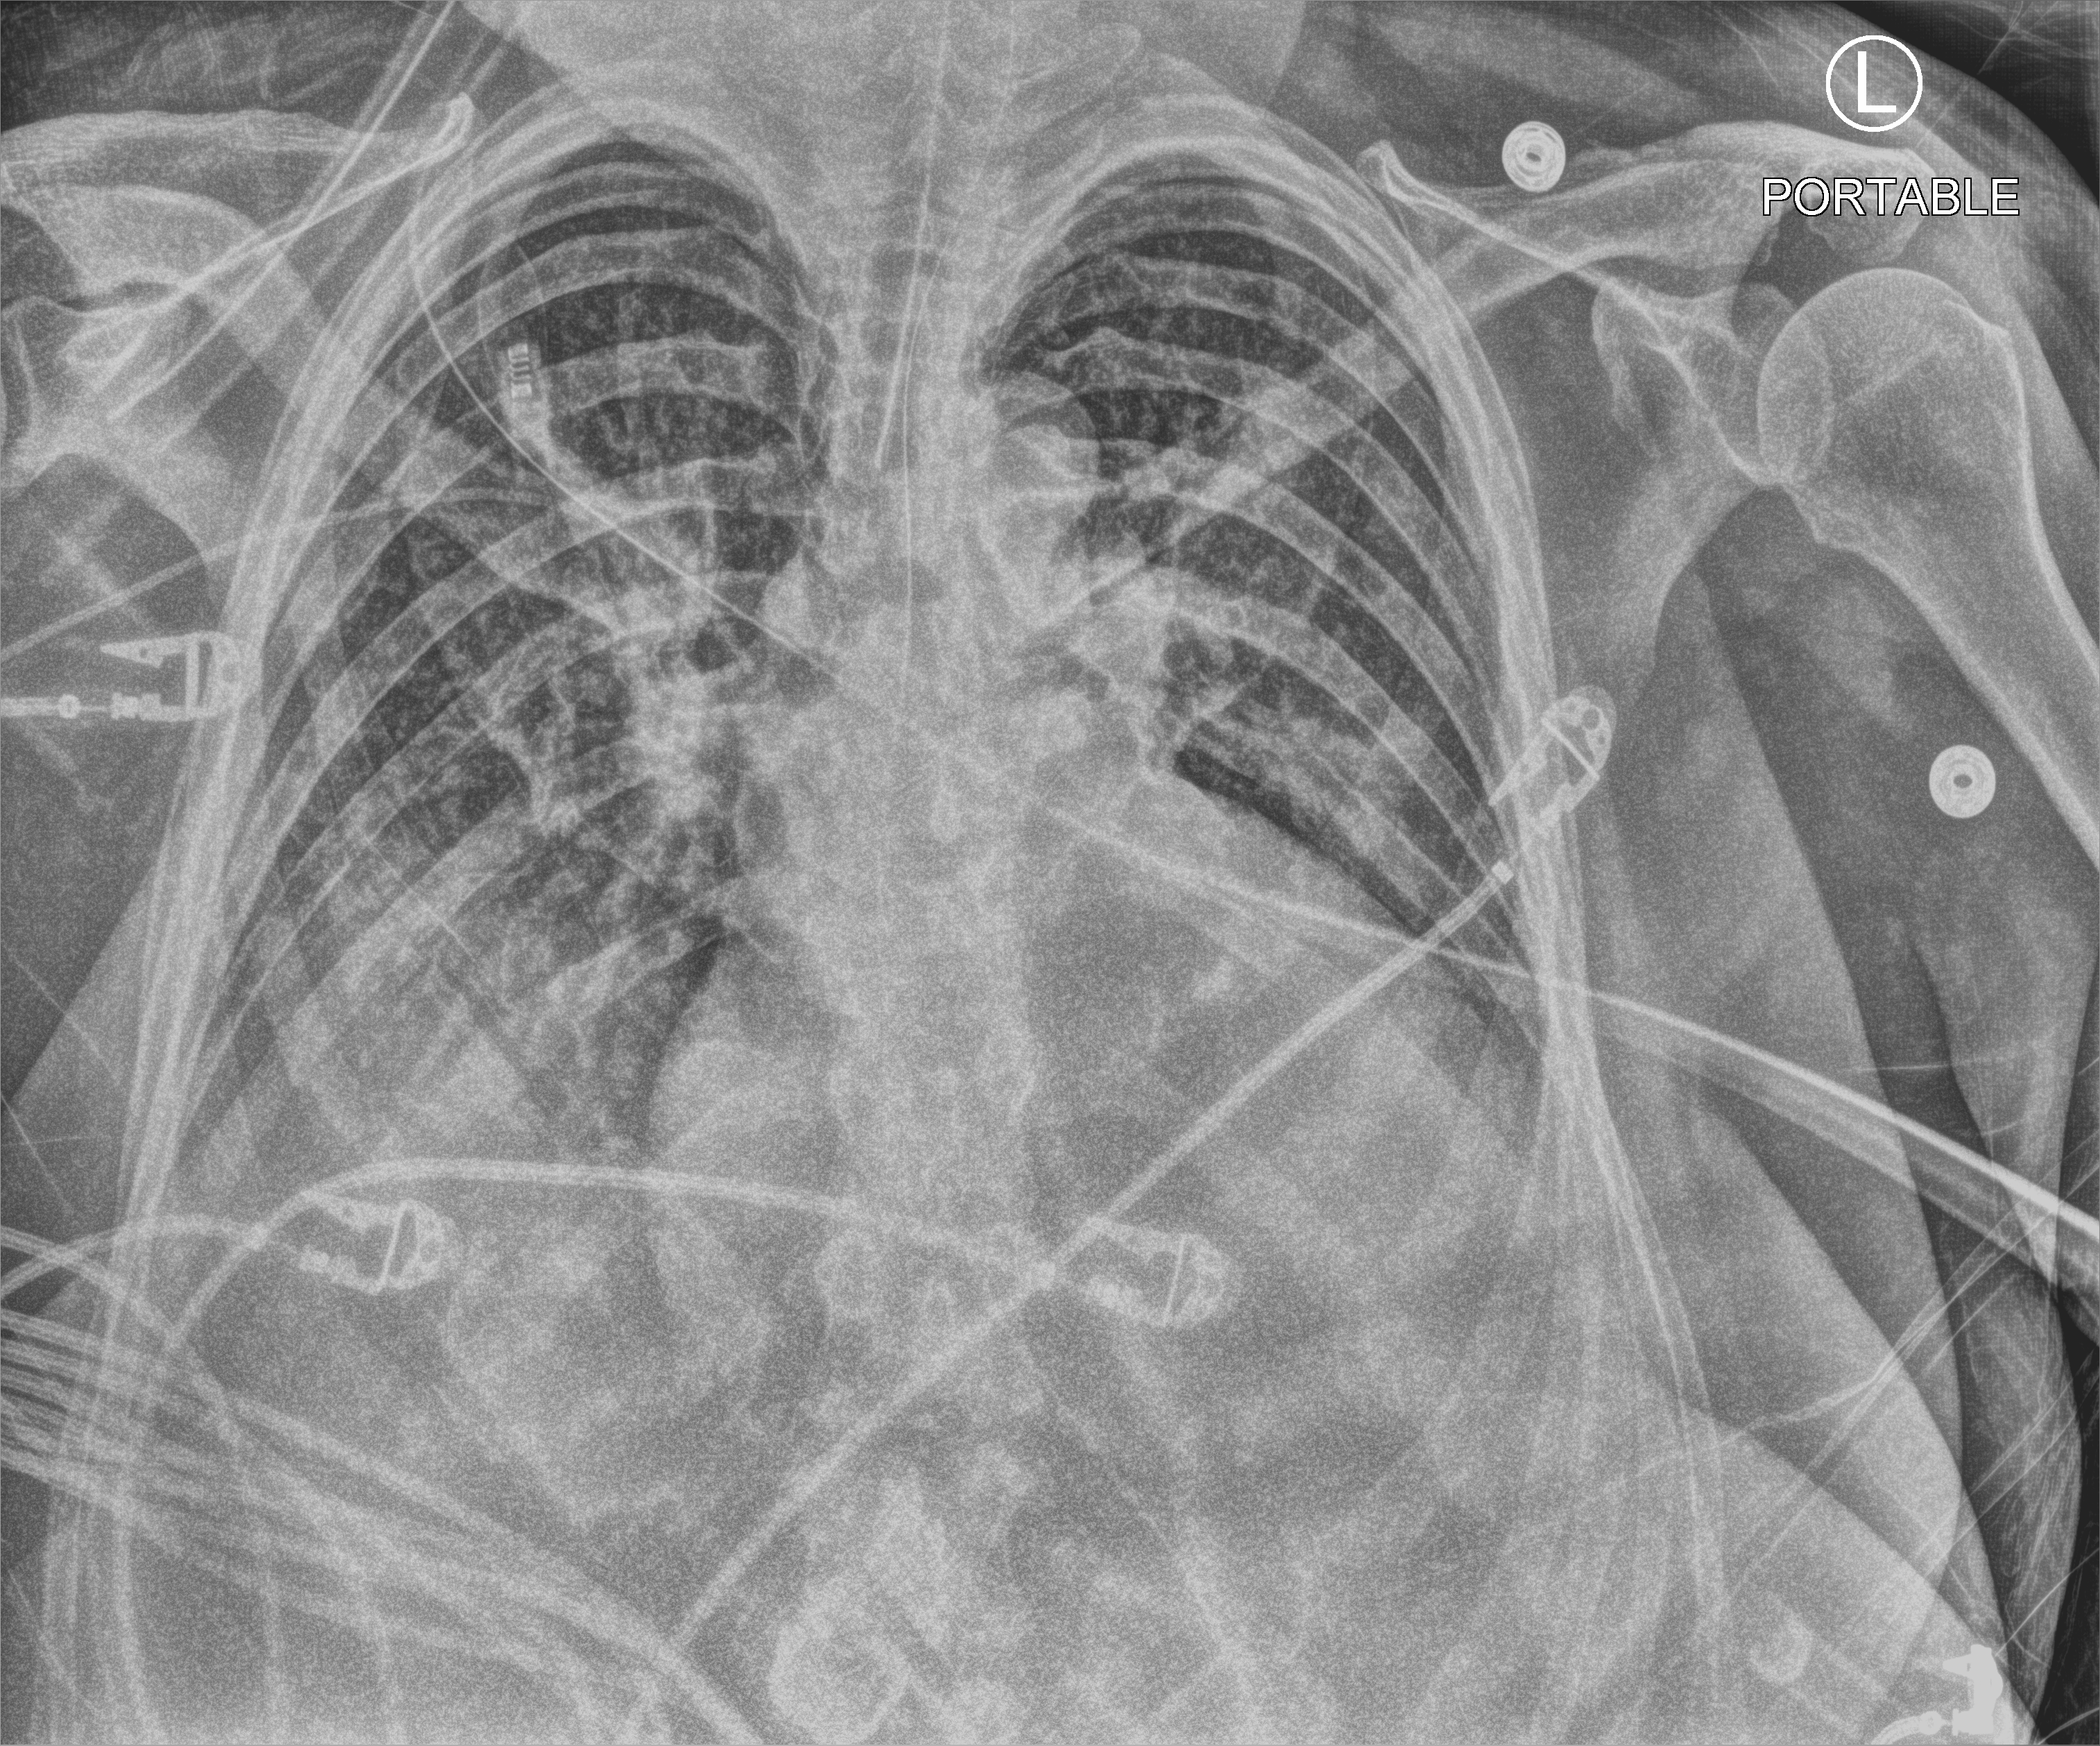
Portable chest radiograph. Female patient hospitalised with COVID-19, age 60–74 years.
Admission-level facts for this patient (not findings on this image; timing relative to this image not recorded): admitted to intensive care during this hospital stay: yes.